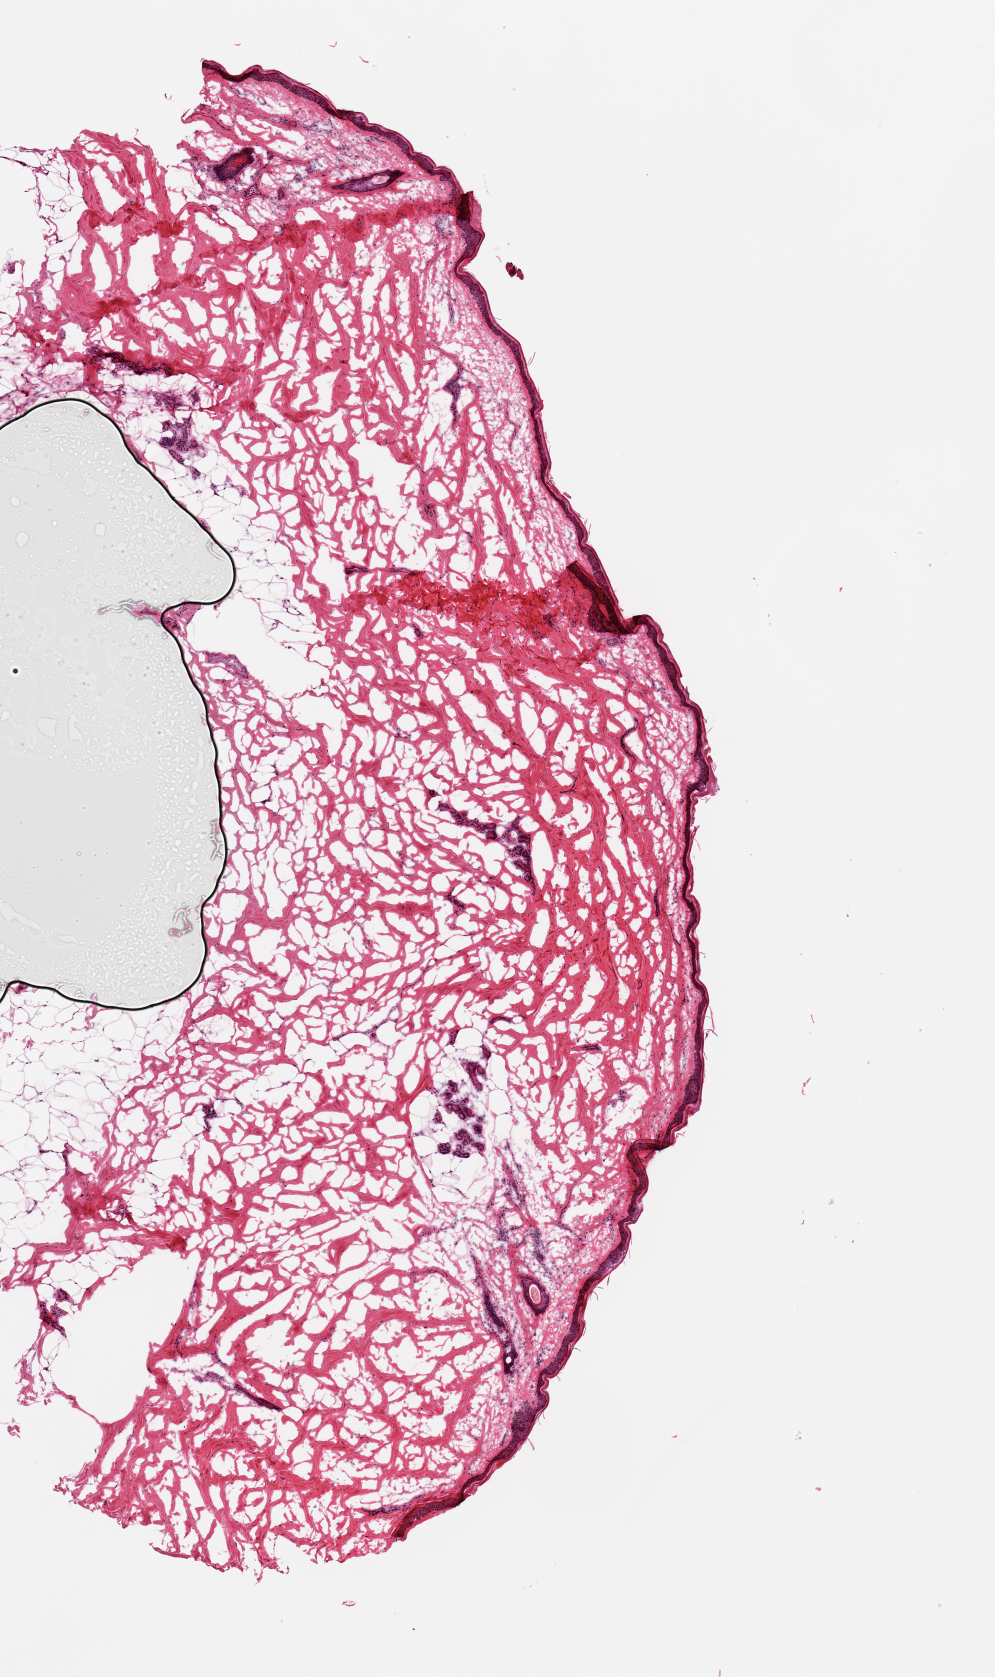
Whole-slide image, haematoxylin and eosin stain — whole scanned area (about 3.9 x 6.6 mm) shown as a low-resolution overview.
Specimen: frozen section (dry ice); sampled site (target tissue): skin of lower leg; tissue donor sample.